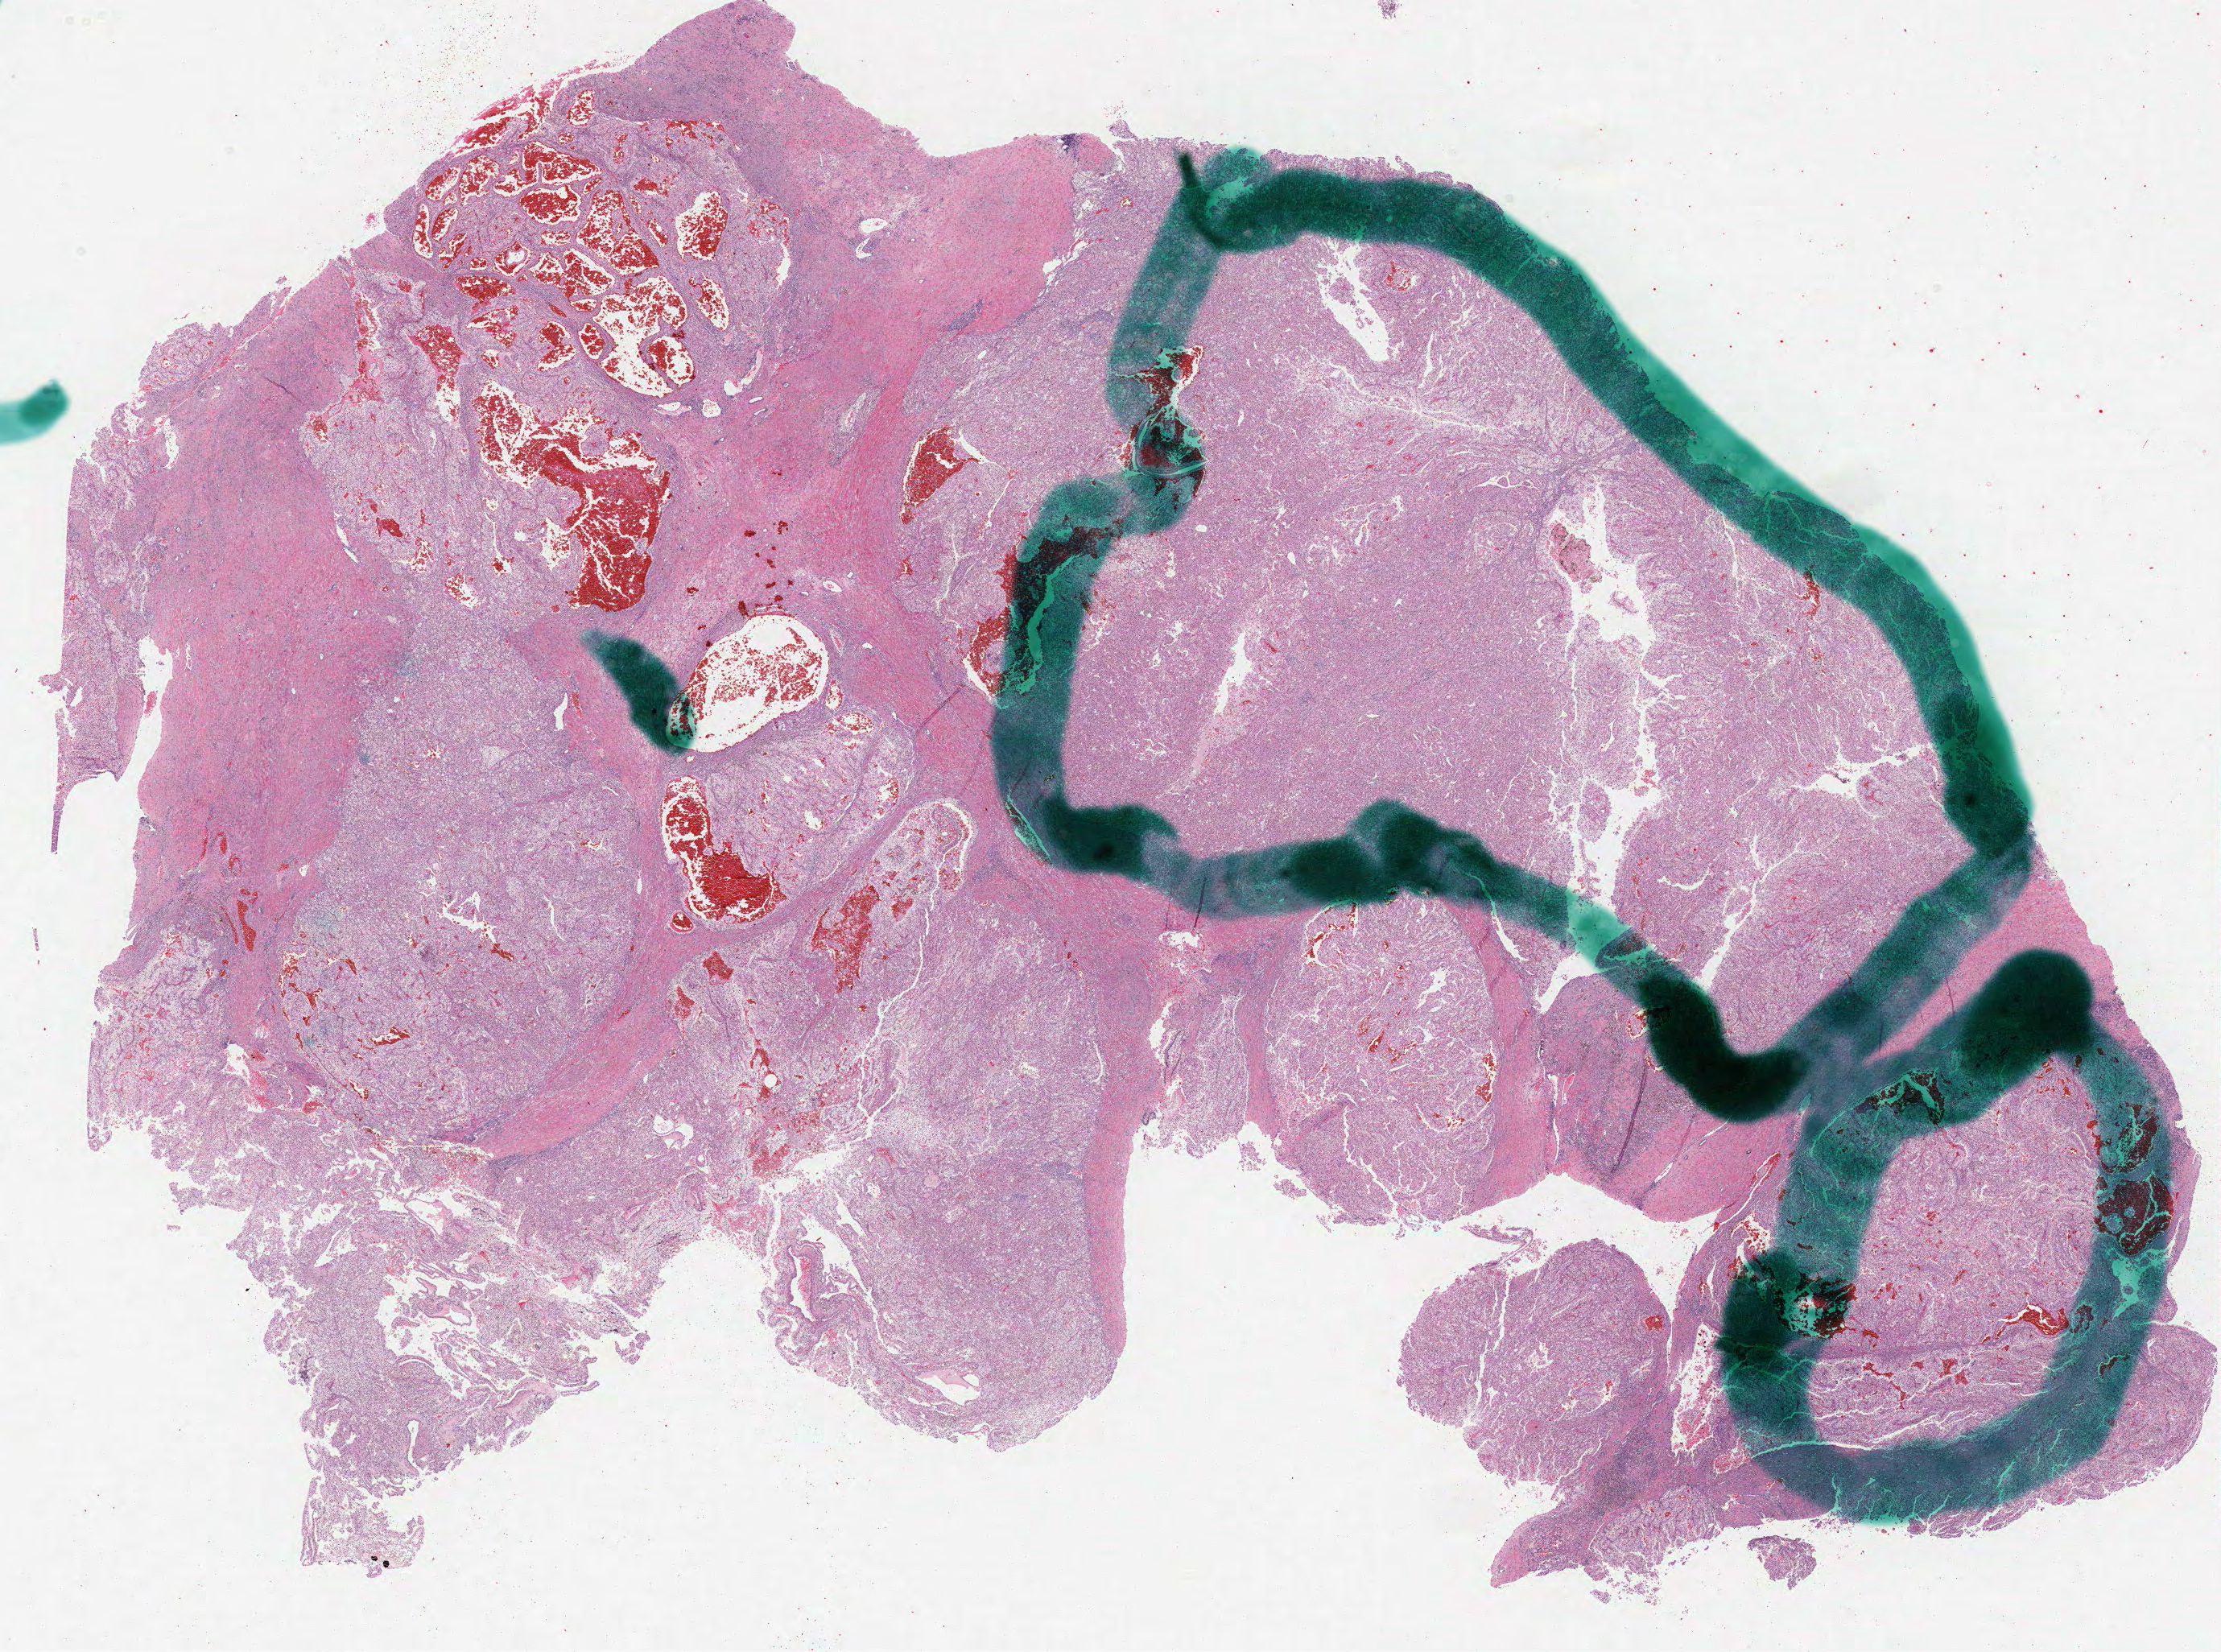
Digitized H&E tissue section (whole slide) — shown as a low-resolution overview of the whole scanned area (about 22.1 x 16.4 mm). Formalin-fixed paraffin-embedded (FFPE) diagnostic section. Kidney, primary tumour sample. Male patient; age at initial diagnosis 64 years.
AJCC pathologic stage: III (6th edition). Lymph nodes positive (case pathology): 0 of 11 examined. TNM: T3a N0 M0. Histologic diagnosis: Papillary adenocarcinoma, NOS.